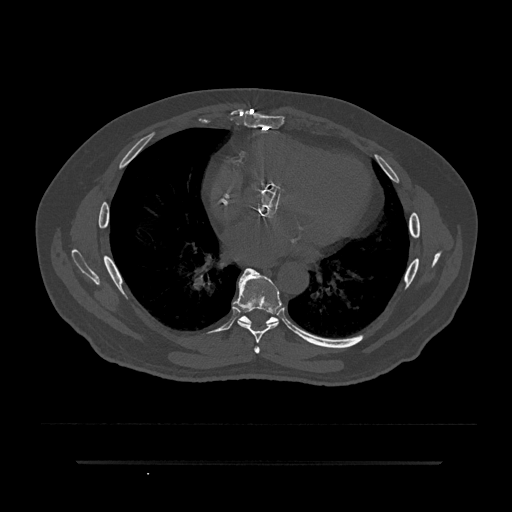
CT including the spine, one axial slice. Slice 461 of 797 in the series (ordered by position). Reconstruction kernel Br40s/3. Bone window (W 1800 / L 400 HU). 0.5 mm slice thickness. 512 × 512 image matrix, field of view 464 × 464 mm. Male patient, age 59 years. Case-level facts recorded for this patient, not image findings: primary cancer: bile ducts; vertebrae with lytic lesions (as recorded): T10.
Outlined on this slice (semi-automatic segmentation, software-assisted and operator-edited):
- T6 vertebra: box from (x=254, y=346) to (x=260, y=353) px
- T7 vertebra: (x=233, y=268)–(x=282, y=343)
- T8 vertebra: (x=225, y=309)–(x=297, y=334)